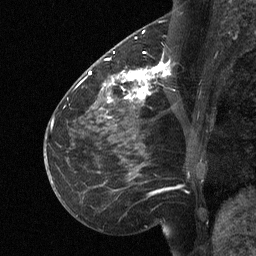
Breast MRI (dynamic contrast-enhanced), one sagittal slice. Slice 25 of 64 in the series (ordered by position). Dynamic contrast-enhanced study with each time point stored as its own series, time point 2 of 3 at this slice position (early post-contrast, ordered by acquisition time). 1.5 T. TE 4.8 ms, TR 27 ms. 2 mm slice thickness. 256 × 256 image matrix, field of view 200 × 200 mm. Patient: female, 51 years. From the clinical record (not read from this slice): setting: breast cancer imaged before/during neoadjuvant chemotherapy; receptor status: HR-positive, HER2-negative.
Outlined on this slice (semi-automatically segmented with operator editing):
- analysis volume of interest (the breast-tissue region the enhancement analysis was run in; not a lesion): box from (x=112, y=46) to (x=169, y=106) px
- tumour enhancement mask (voxels above the 90 % enhancement threshold inside the analysis volume of interest): (x=112, y=52)–(x=169, y=101)